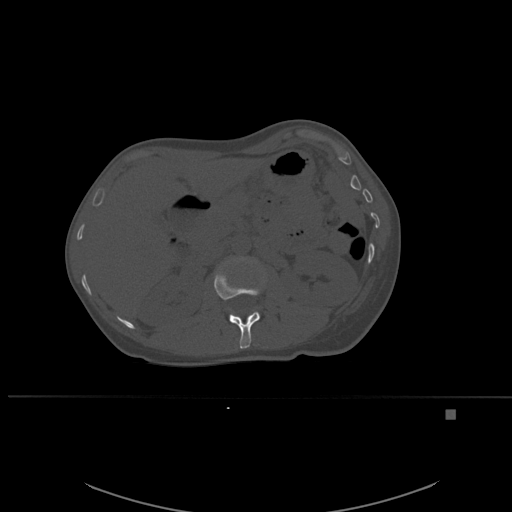
CT including the spine, one axial slice; slice 252 of 537 in the series (ordered by position); bone window (W 1800 / L 400 HU); 1.5 mm slice thickness; 512 × 512 image matrix, field of view 440 × 440 mm. Female patient, age 45 years. Case-level facts recorded for this patient, not image findings: primary cancer: lung.
Annotated regions visible in this slice (semi-automatic segmentation, software-assisted and operator-edited):
- L1 vertebra: bounding box <214,263,260,349> (left, top, right, bottom; pixels)
- L2 vertebra: <234,257,250,262>